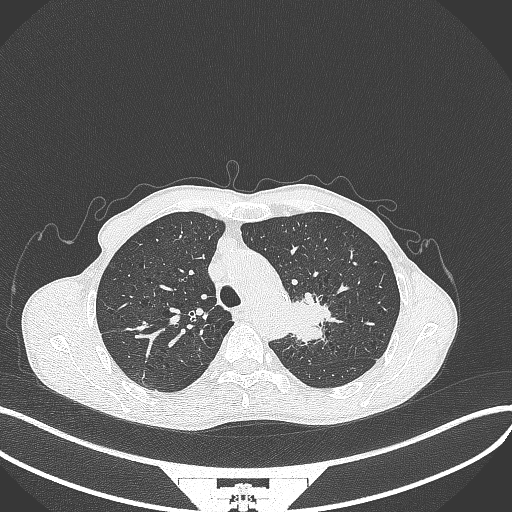
Chest CT, one axial slice; slice 313 of 386 in the series (ordered by position); reconstruction kernel B70f; lung window (W 1500 / L -600 HU); 1 mm slice thickness; 512 × 512 image matrix. Male patient, age 65 years. Case-level facts recorded for this patient, not image findings: clinical TNM (as recorded): T2b N0 M0; histopathological grade: G2.
Outlined on this slice (bounding box drawn by a radiologist):
- lung tumour (recorded histology: adenocarcinoma): box from (x=287, y=286) to (x=337, y=346) px